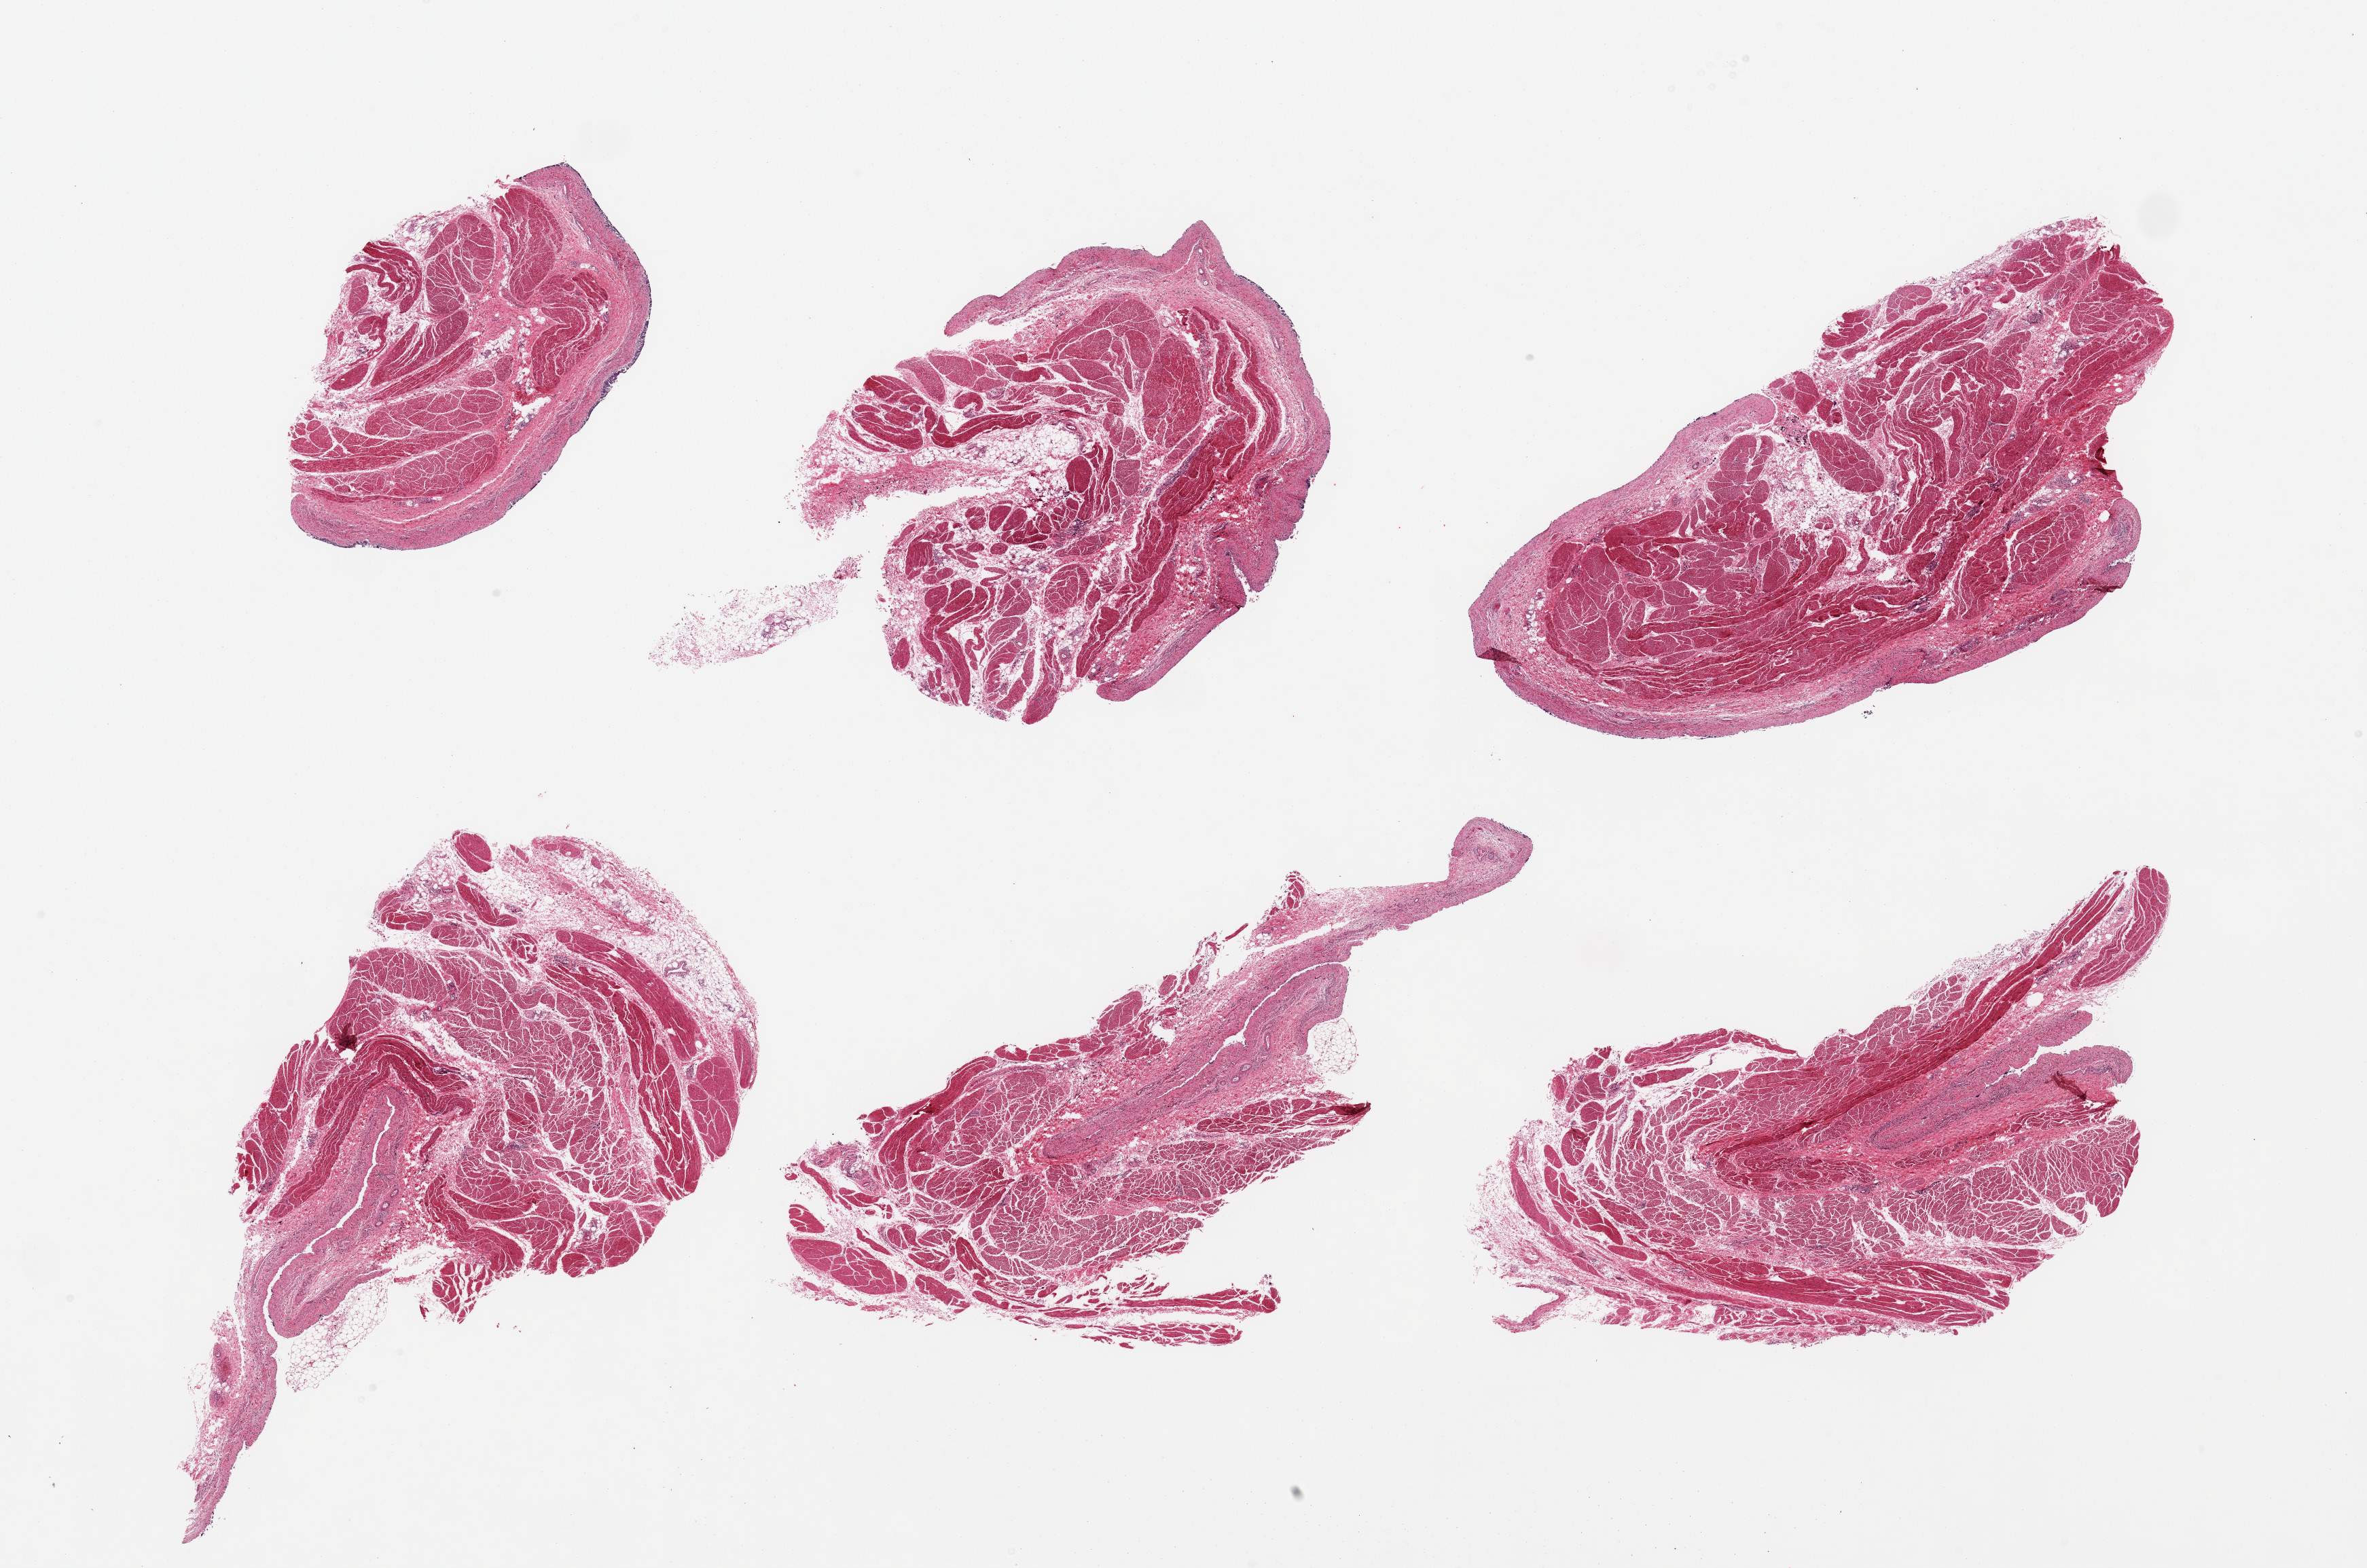
Haematoxylin and eosin whole-slide image — whole scanned area (about 27.6 x 18.3 mm, from a 20x scan) shown as a low-resolution overview; PAXgene-fixed, paraffin-embedded tissue; sampled site (target tissue): vagina; donor tissue sample. Donor sex: female.
* reviewer comment on this tissue sample: 6 pieces; urinary bladder sampled, not vagina